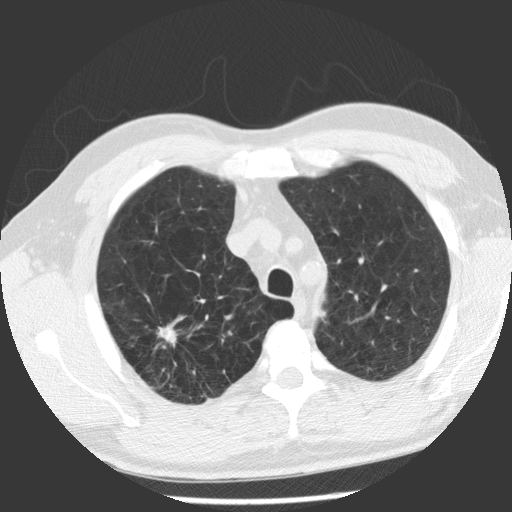
Axial slice from a low-dose chest CT screening exam. Baseline annual screen. Lung window (W 1500 / L -600 HU). 140 kVp. Slice 89 of 112 in the series. 512 × 512 image matrix, field of view 344 × 344 mm. Male, age 62 years at enrolment. Former smoker at enrolment.
Expert reader's lesion annotation, bounding box [x1, y1, x2, y2] px = [120, 302, 200, 383]. The screening reader recorded 2 non-calcified nodules or masses ≥4 mm on this exam (right upper lobe, right upper lobe); which of them this box marks is not recorded. Official screen result: positive, change unspecified: nodule(s) >= 4 mm or enlarging nodule(s), mass(es), or other non-specific abnormalities suspicious for lung cancer. Participant outcome: lung cancer diagnosed 71 days after this screen — adenocarcinoma, NOS, right upper lobe, poorly differentiated (G3), stage IV (AJCC 6th edition), 30 mm at pathology.